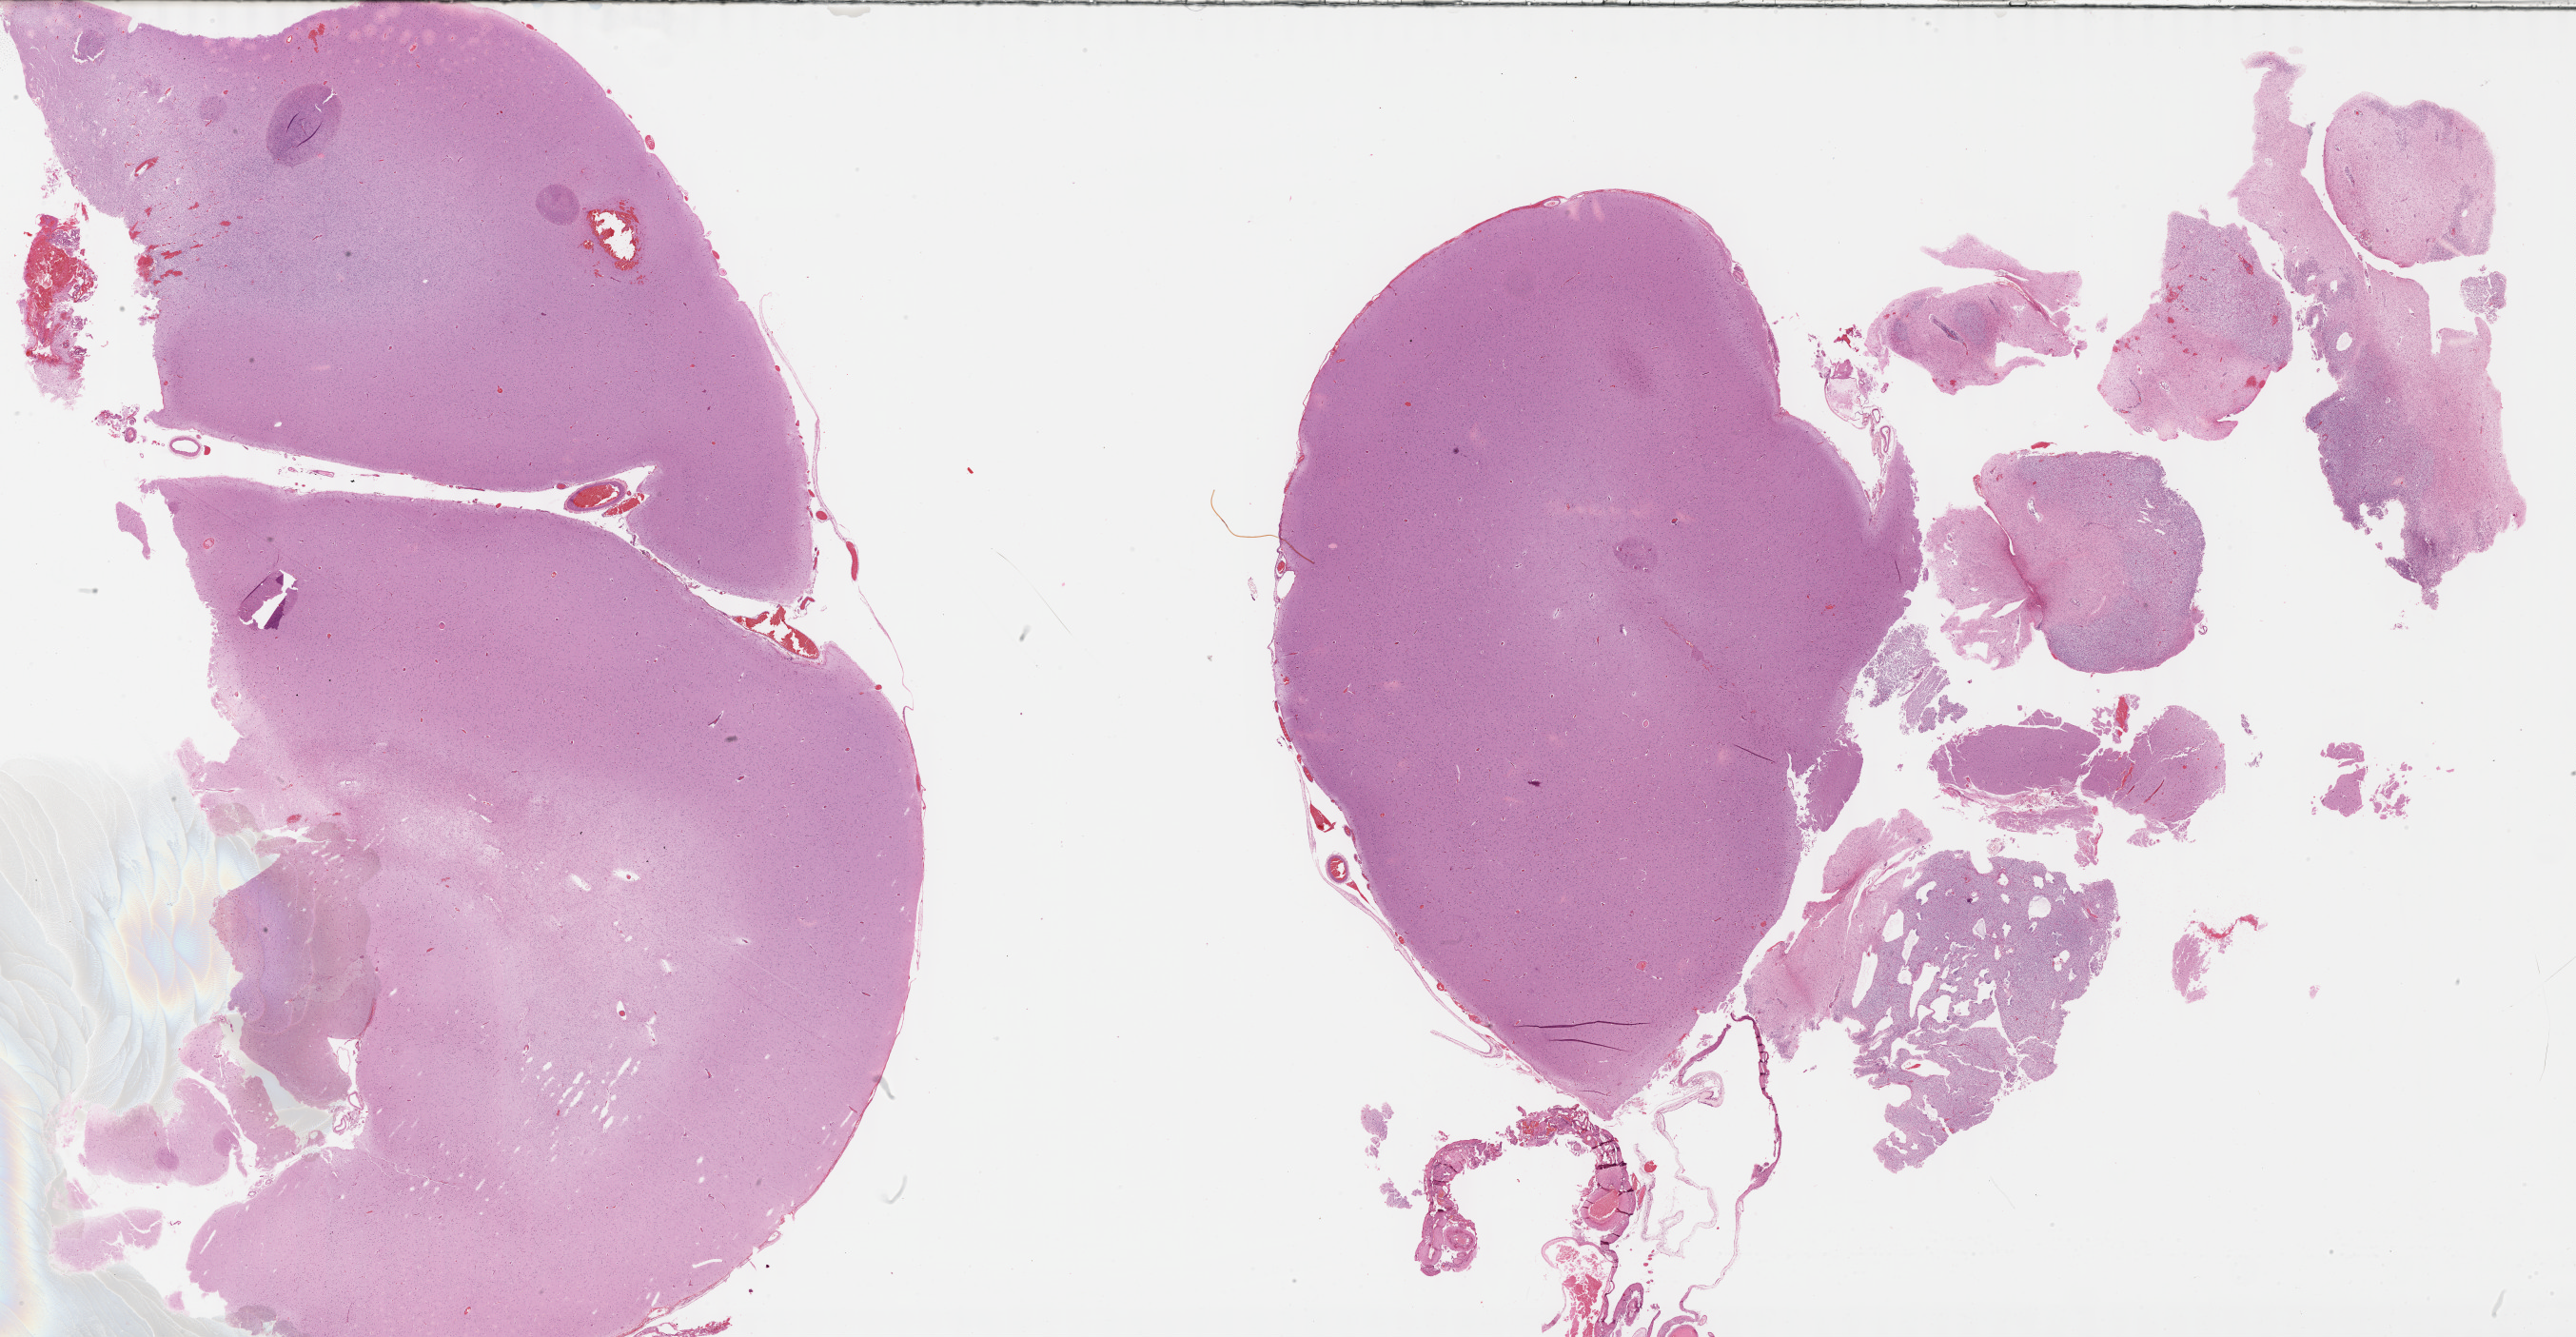
Digitized Hematoxylin and eosin (H&E) stained tissue section (whole slide) — whole scanned area (about 43.8 x 22.7 mm) shown as a low-resolution overview. Formalin-fixed paraffin-embedded (FFPE) diagnostic section. Sample: primary tumour, brain. Male, age 51 years at initial diagnosis. Histologic grade: G2 (moderately differentiated).
Laterality: left. Histologic diagnosis: Oligodendroglioma, NOS.